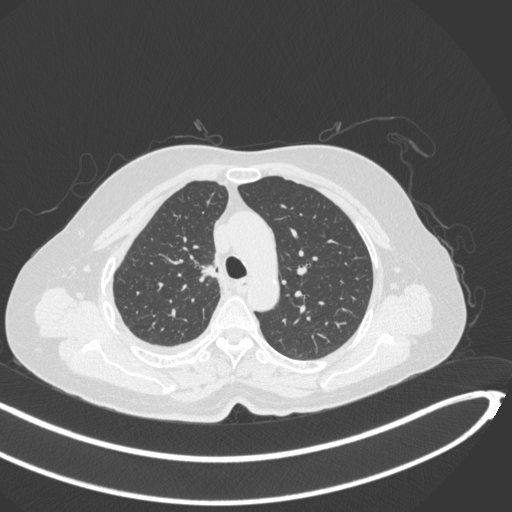
Chest CT, one axial slice. Slice 220 of 297 in the series (ordered by position). 120 kVp. Lung window (W 1500 / L -600 HU). 1 mm slice thickness. 512 × 512 image matrix, field of view 400 × 400 mm. Female patient, age 64 years. Case-level facts recorded for this patient, not image findings: clinical TNM (as recorded): T1b N0 M1.
Structures marked on this image (bounding box drawn by a radiologist):
- lung tumour (recorded histology: adenocarcinoma): bounding box (x1, y1, x2, y2) in pixels: (194, 259, 218, 289)